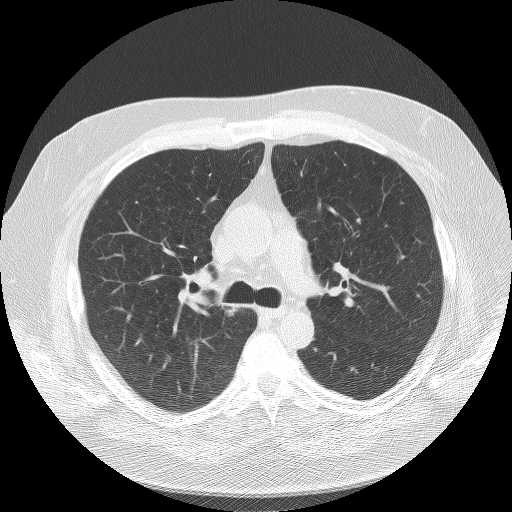
Low-dose screening chest CT, axial slice, third annual screen, lung window (W 1500 / L -600 HU), slice 44 of 136 in the series, 512 × 512 image matrix, field of view 360 × 360 mm. Male, age 58 years at enrolment. Former smoker at enrolment.
Expert-annotated lung lesion, box from (x=206, y=287) to (x=254, y=337) px. The exam's reader record, not a measurement of the box and not confirmed to be the same lesion: non-calcified nodule or mass ≥4 mm, right upper lobe, 9 × 8 mm, spiculated (stellate) margins, soft tissue attenuation, pre-existing on the prior screen: yes; interval growth: yes. Official screen result: positive, other.